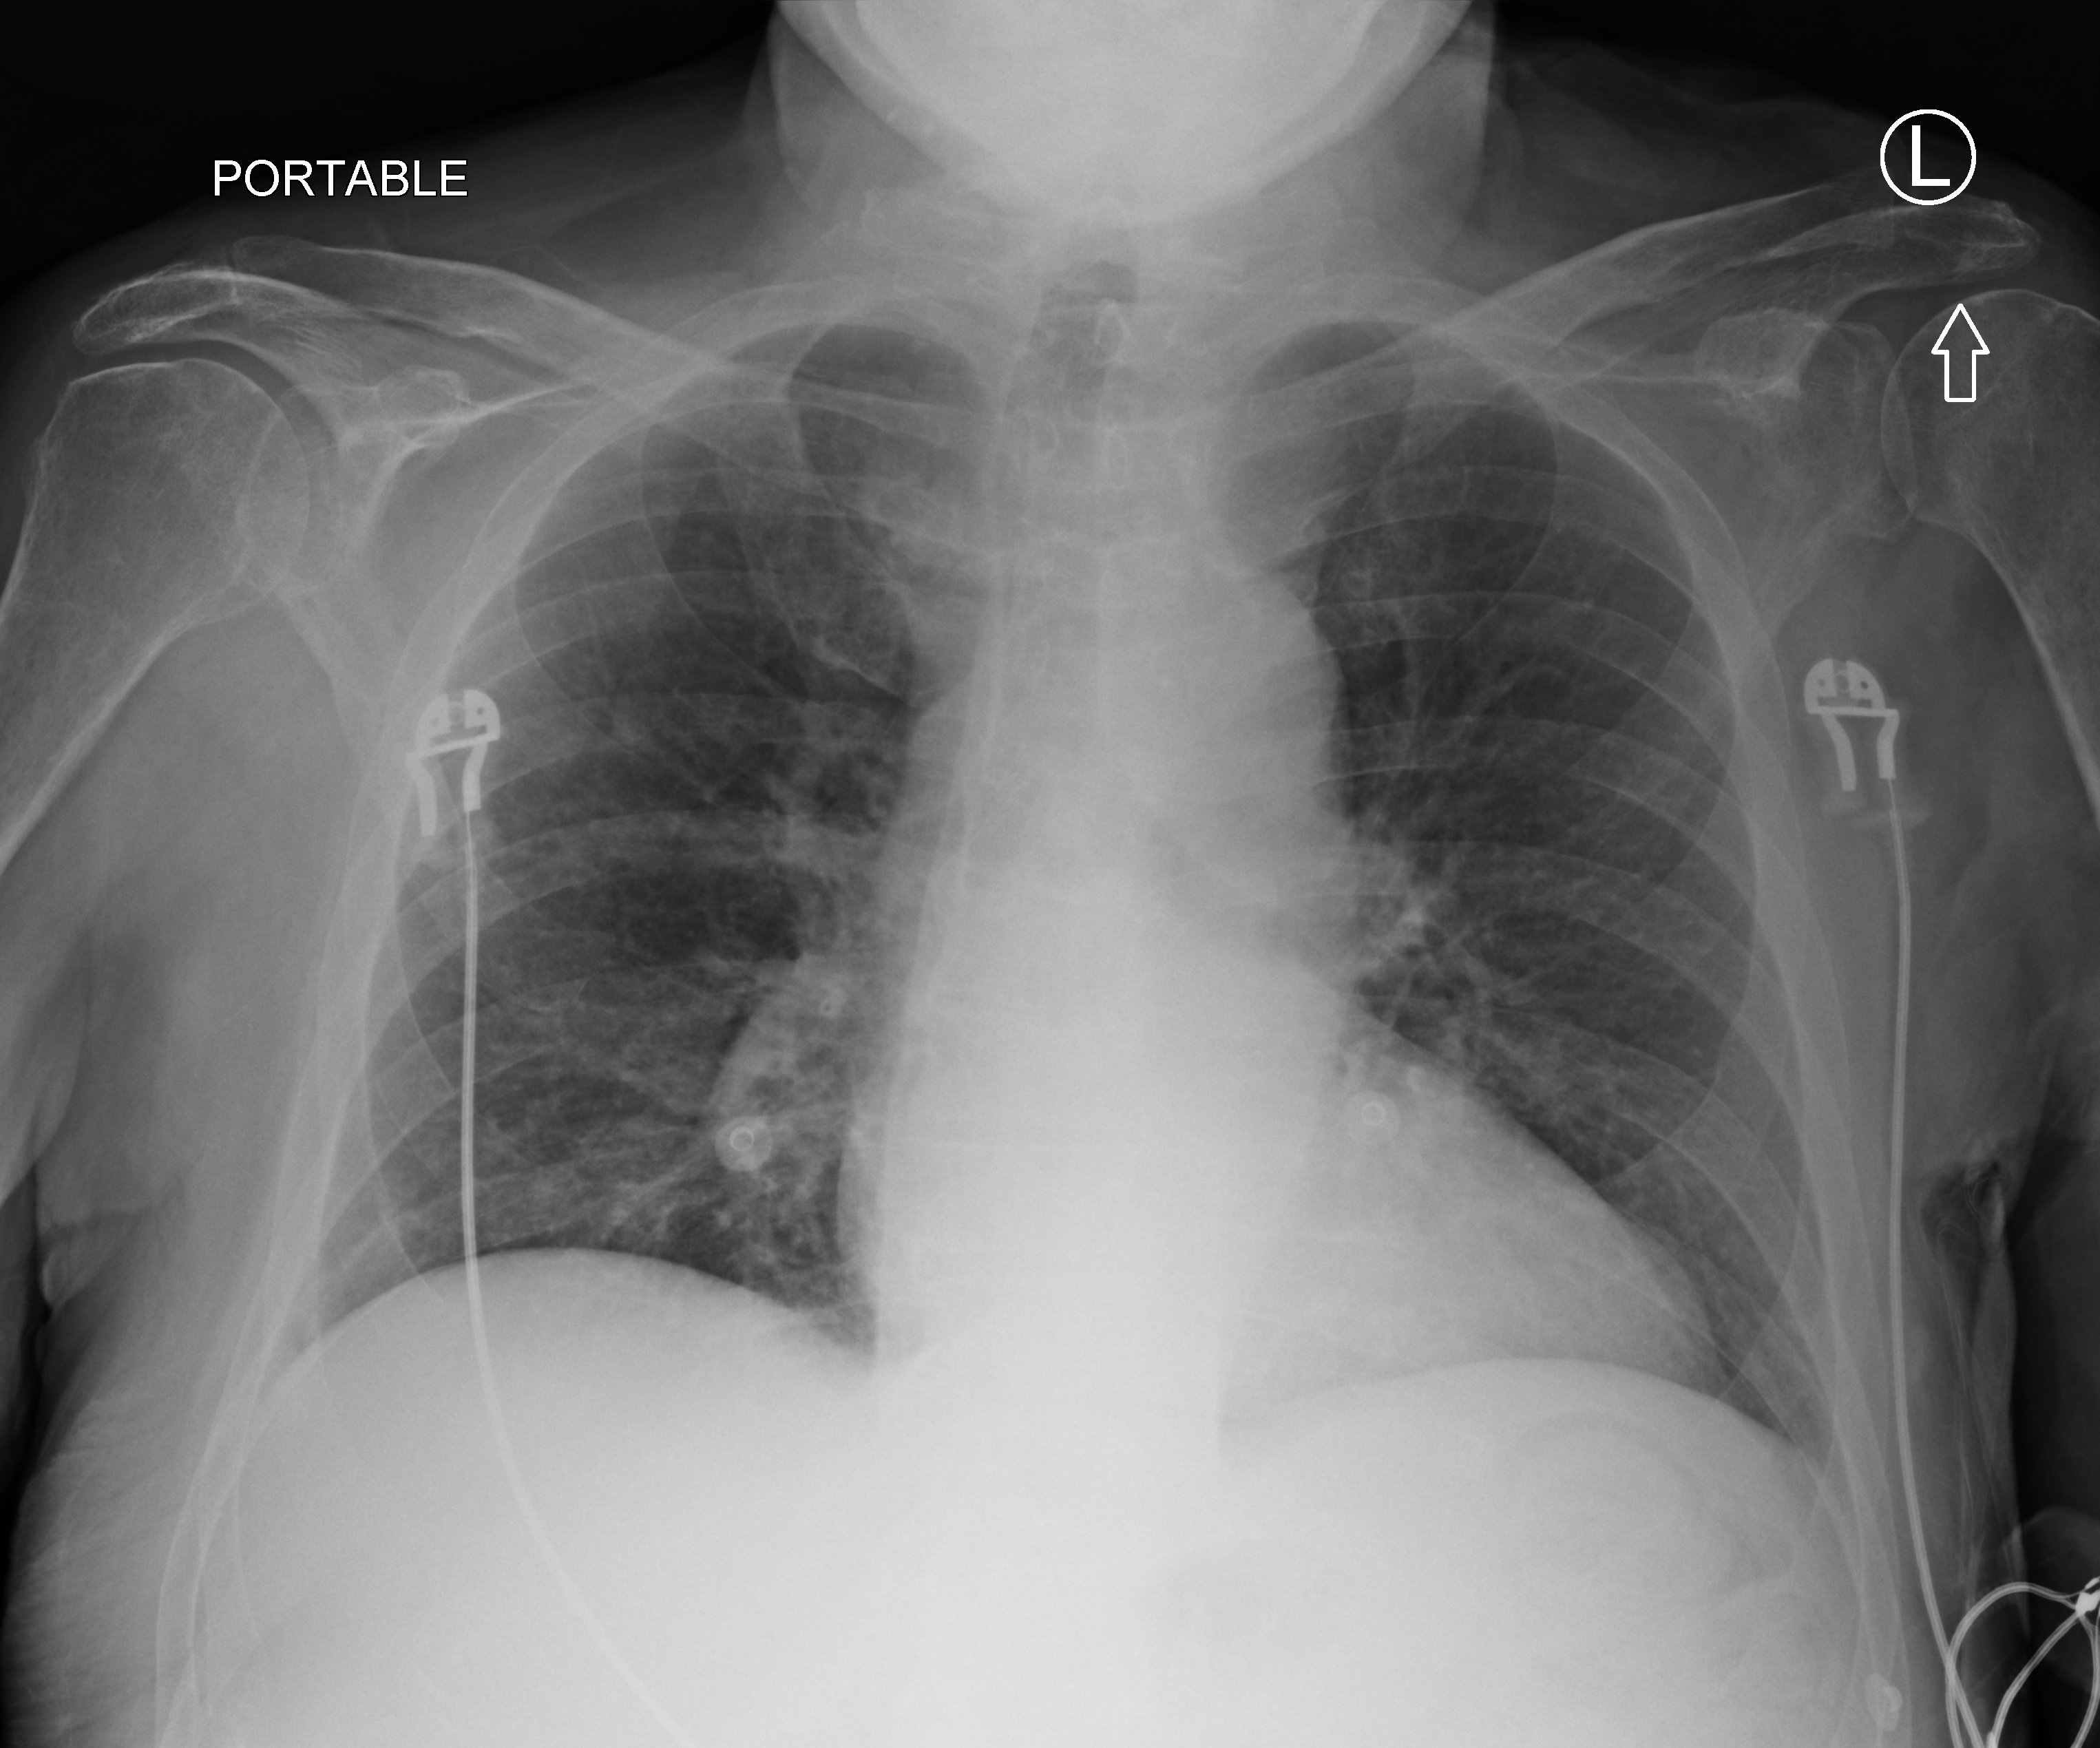
Portable chest radiograph, anteroposterior (AP) projection. Patient hospitalised with COVID-19; male, aged 60–74 years.
Admission-level facts for this patient (not findings on this image; timing relative to this image not recorded): mechanically ventilated during this hospital stay: no; admitted to intensive care during this hospital stay: no; chronic kidney disease (admission record): no.